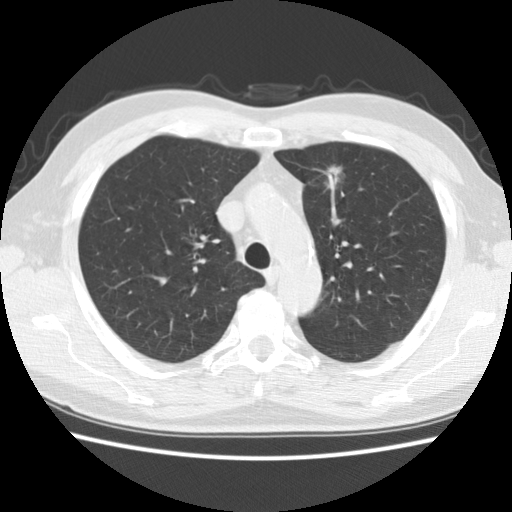
Axial slice from a low-dose chest CT screening exam, second annual screen, lung window (W 1500 / L -600 HU), 2.5 mm slice thickness, standard (soft-tissue) reconstruction kernel (STANDARD). Male, age 63 years at enrolment. Former smoker at enrolment.
Expert-annotated lung lesion, bounding box [x1, y1, x2, y2] px = [299, 148, 356, 201]. Screening reader's record for this exam (one nodule recorded; not confirmed to be the boxed lesion): non-calcified nodule or mass ≥4 mm, left upper lobe, 23 × 18 mm, spiculated (stellate) margins, soft tissue attenuation, pre-existing on the prior screen: yes; interval growth: yes. Official screen result: positive, other. Participant outcome: lung cancer diagnosed 83 days after this screen — adenocarcinoma, NOS, left upper lobe, moderately differentiated (G2), stage IA (AJCC 6th edition), 14 mm at pathology.